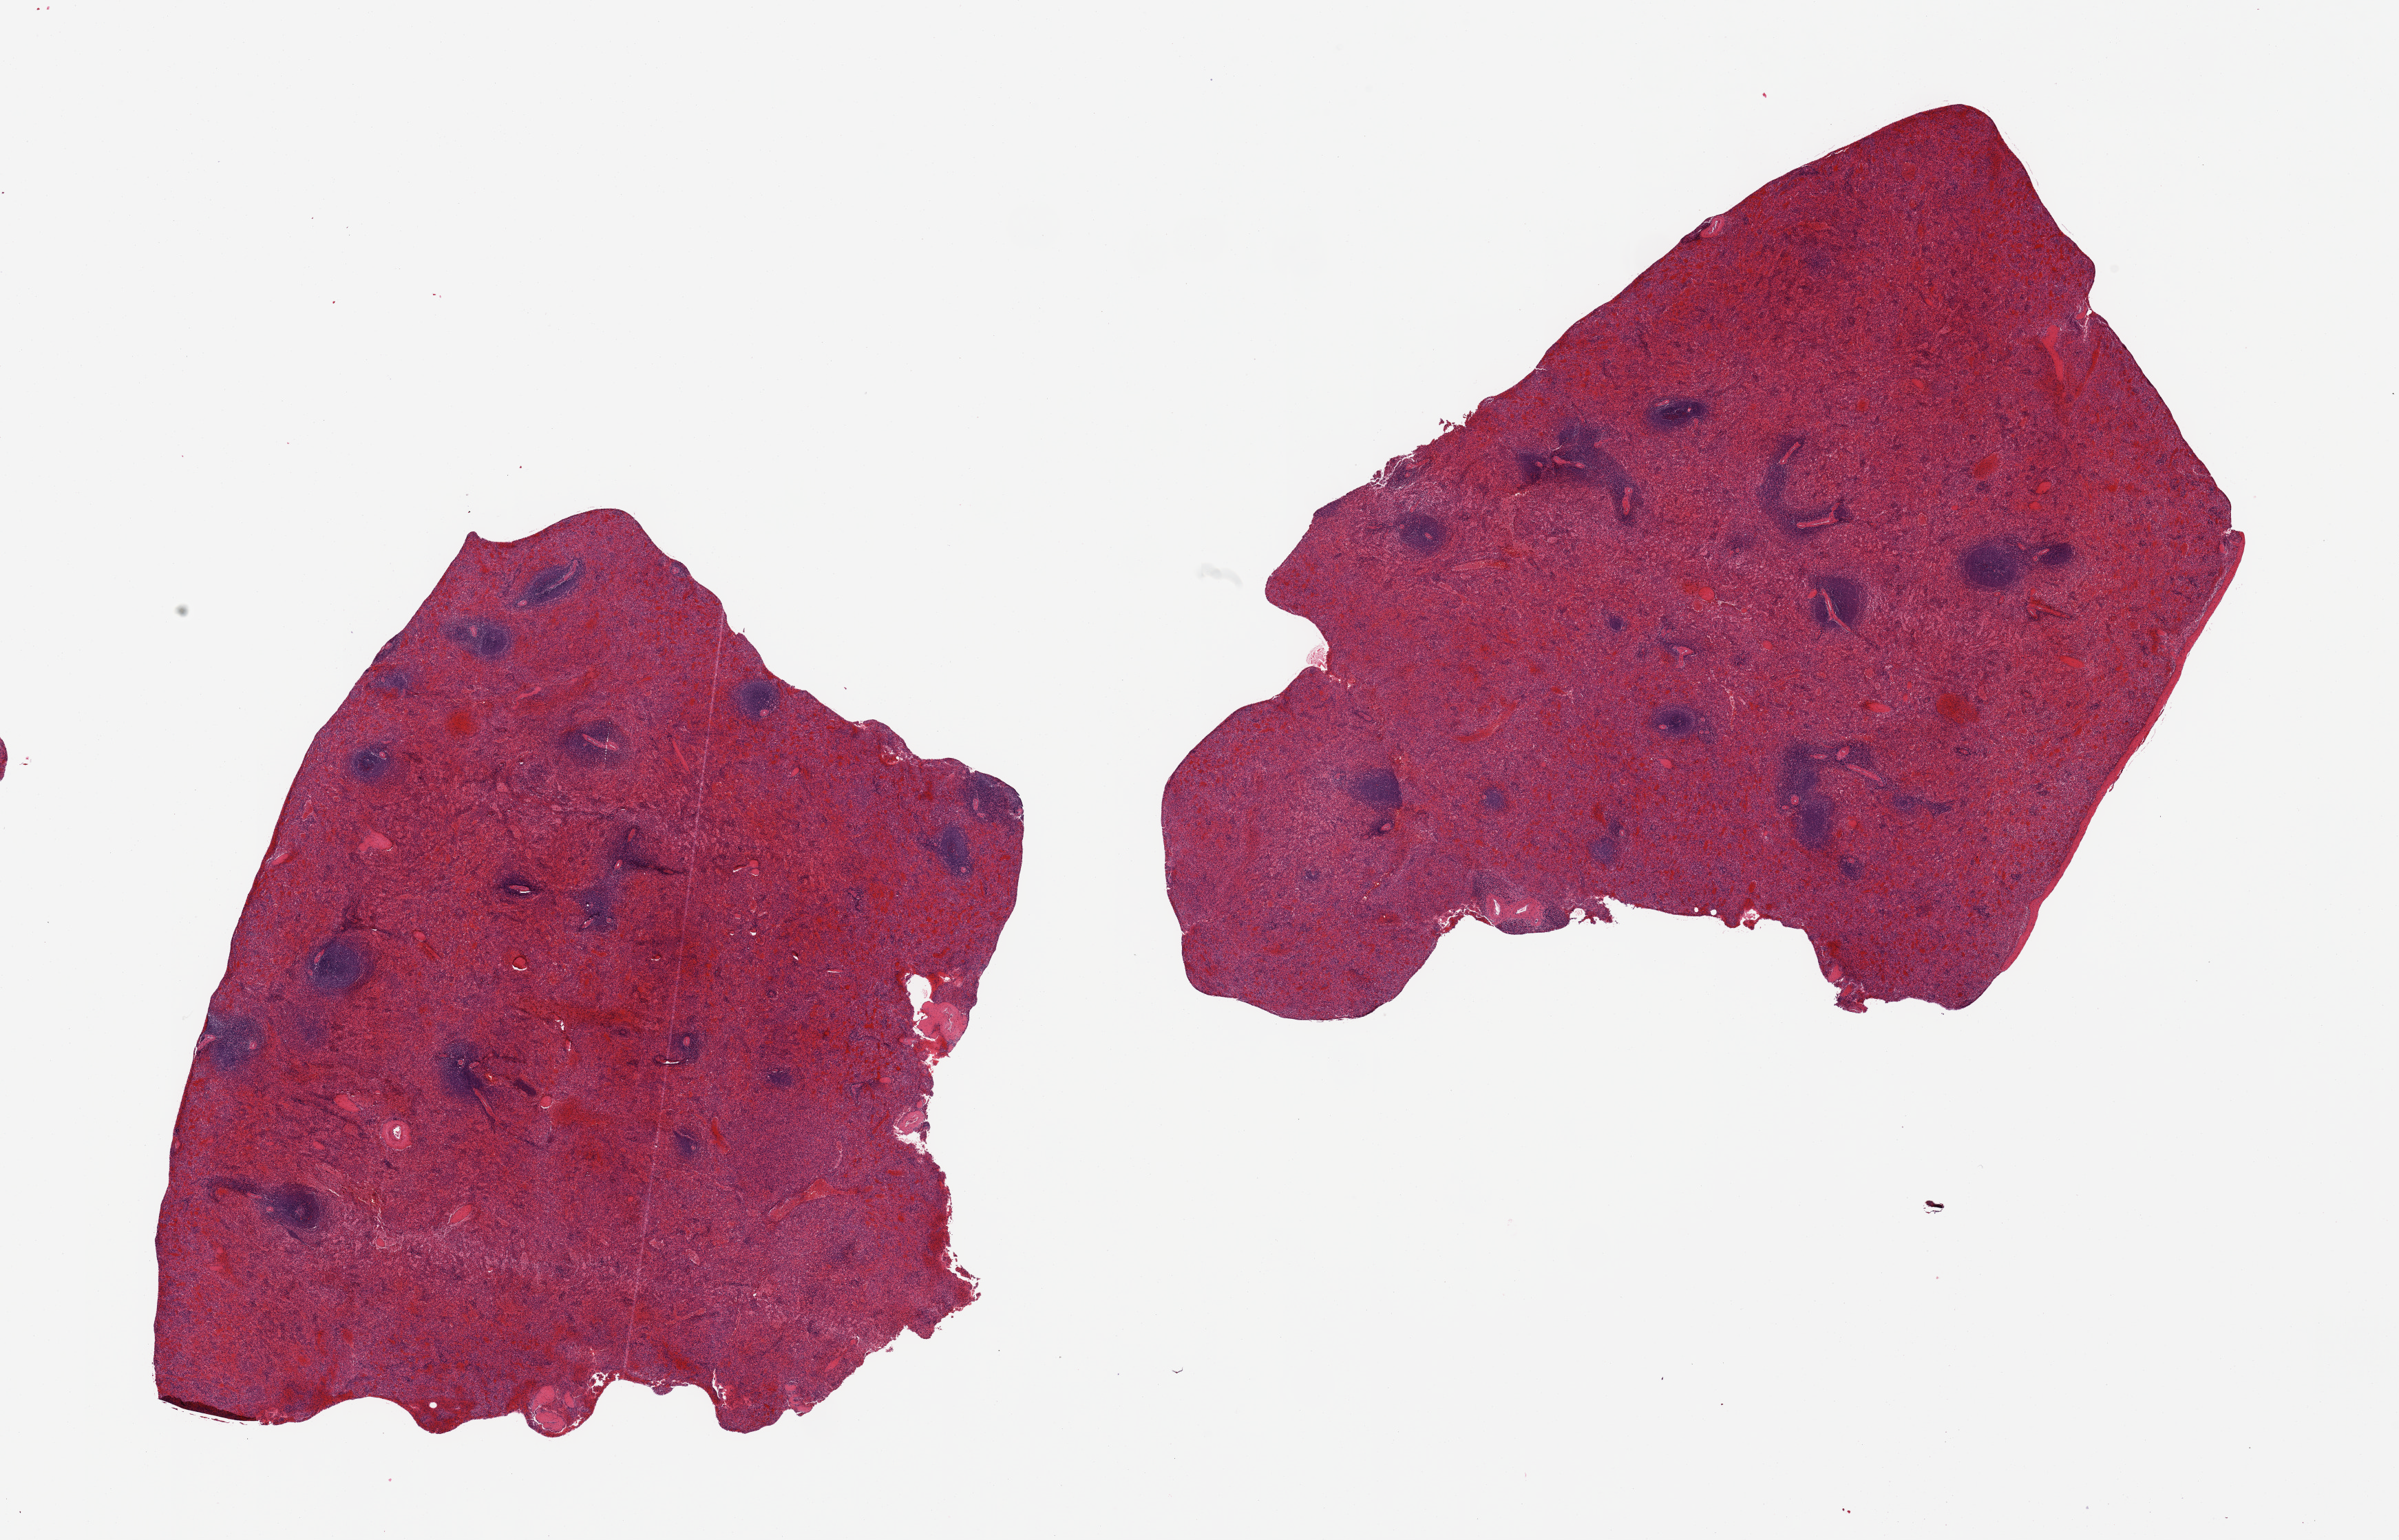
Digitized hematoxylin and eosin (H&E)-stained section — low-resolution overview of the scanned area, about 27.6 x 17.7 mm (slide scanned at 20x), PAXgene-fixed, paraffin-embedded tissue, target tissue: spleen, tissue donor sample.
Review note (as recorded): 2 pieces; moderately congested.